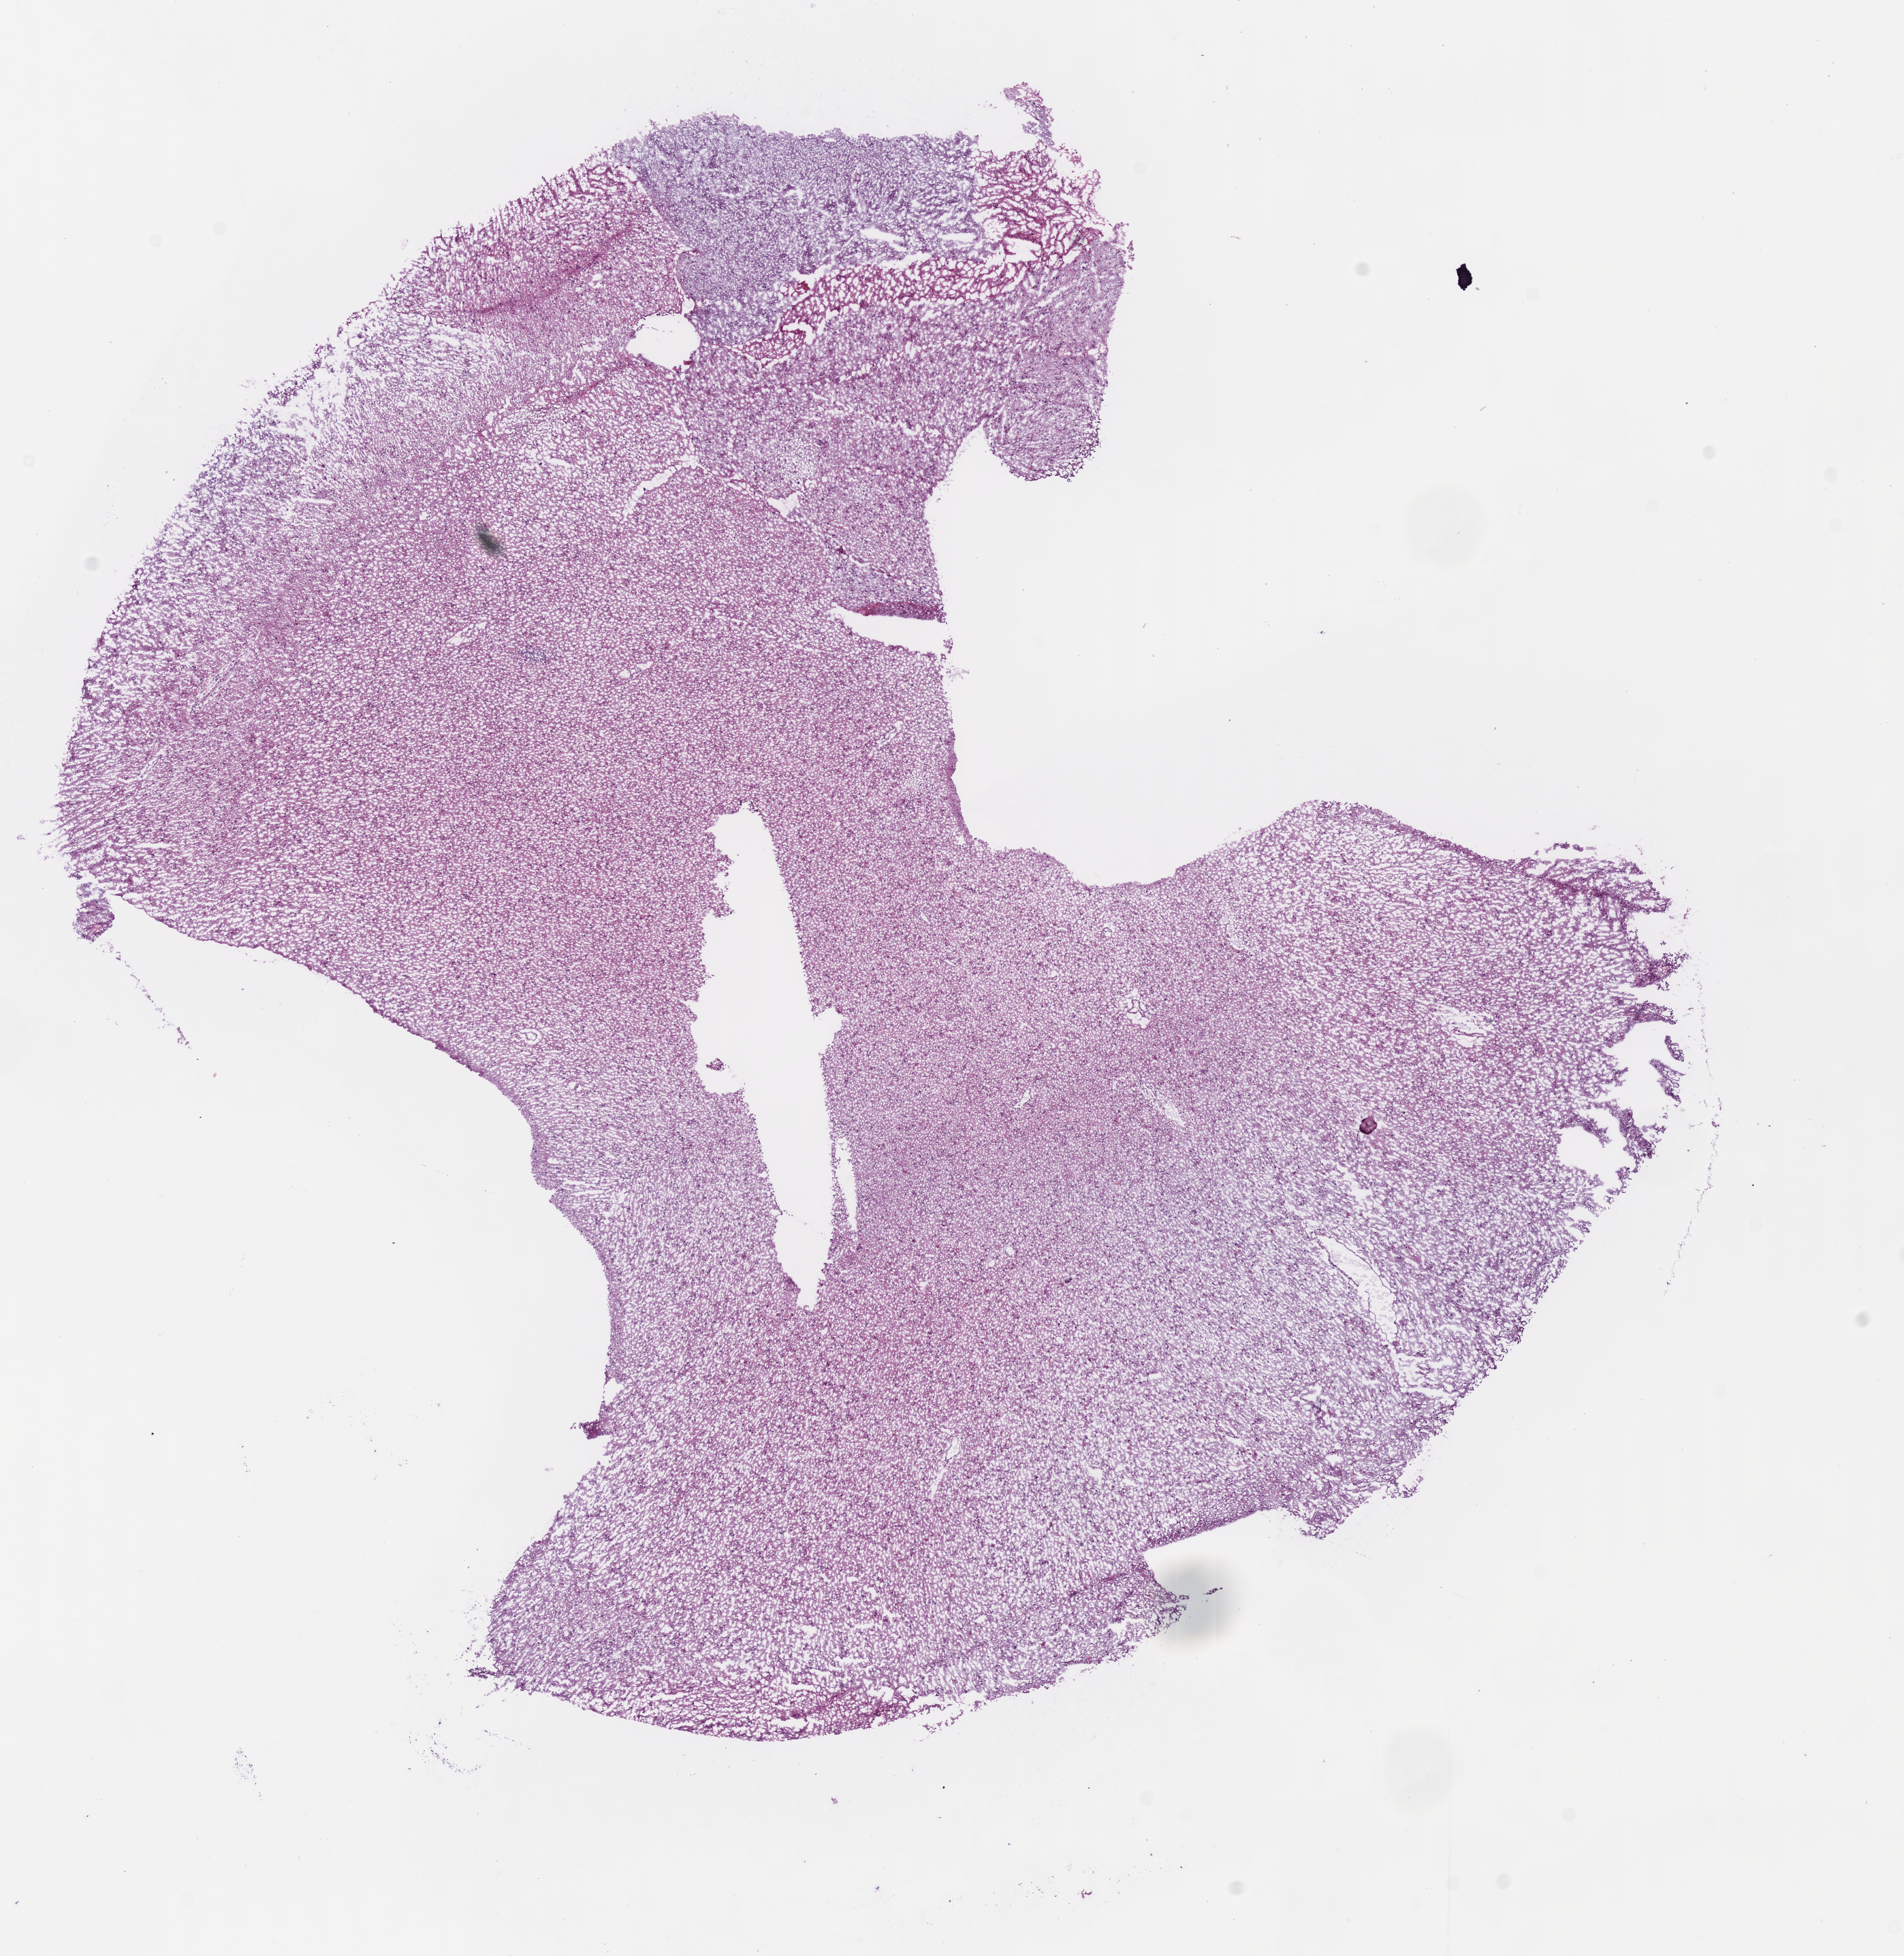
Whole-slide histology image, H&E-stained, shown as a low-resolution overview of the whole scanned area (about 11.0 x 11.3 mm); frozen section from the bottom of the tissue portion; primary tumour sample from the brain. Patient: female, age at initial diagnosis 30 years. Histologic grade: G3 (poorly differentiated). Slide review estimates, as recorded: tumour cells 100%, tumour nuclei 60%, normal cells 0%, stromal cells 0%, necrosis 0%.
Laterality: left. Pathologic diagnosis: Astrocytoma, anaplastic.